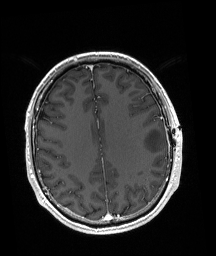
Brain MRI from a brain-tumour surgery series, one axial slice. Slice 69 of 192 in the series (ordered by position). T1-weighted post-contrast. 1 mm slice thickness. 216 × 256 image matrix. From the clinical record (not read from this slice): histopathology: Astrocytoma; WHO grade: 3; IDH mutation: yes; tumour location: Left Posterior Frontal.
Annotated regions visible in this slice (expert manual segmentation):
- tumour: box from (x=141, y=127) to (x=165, y=153) px